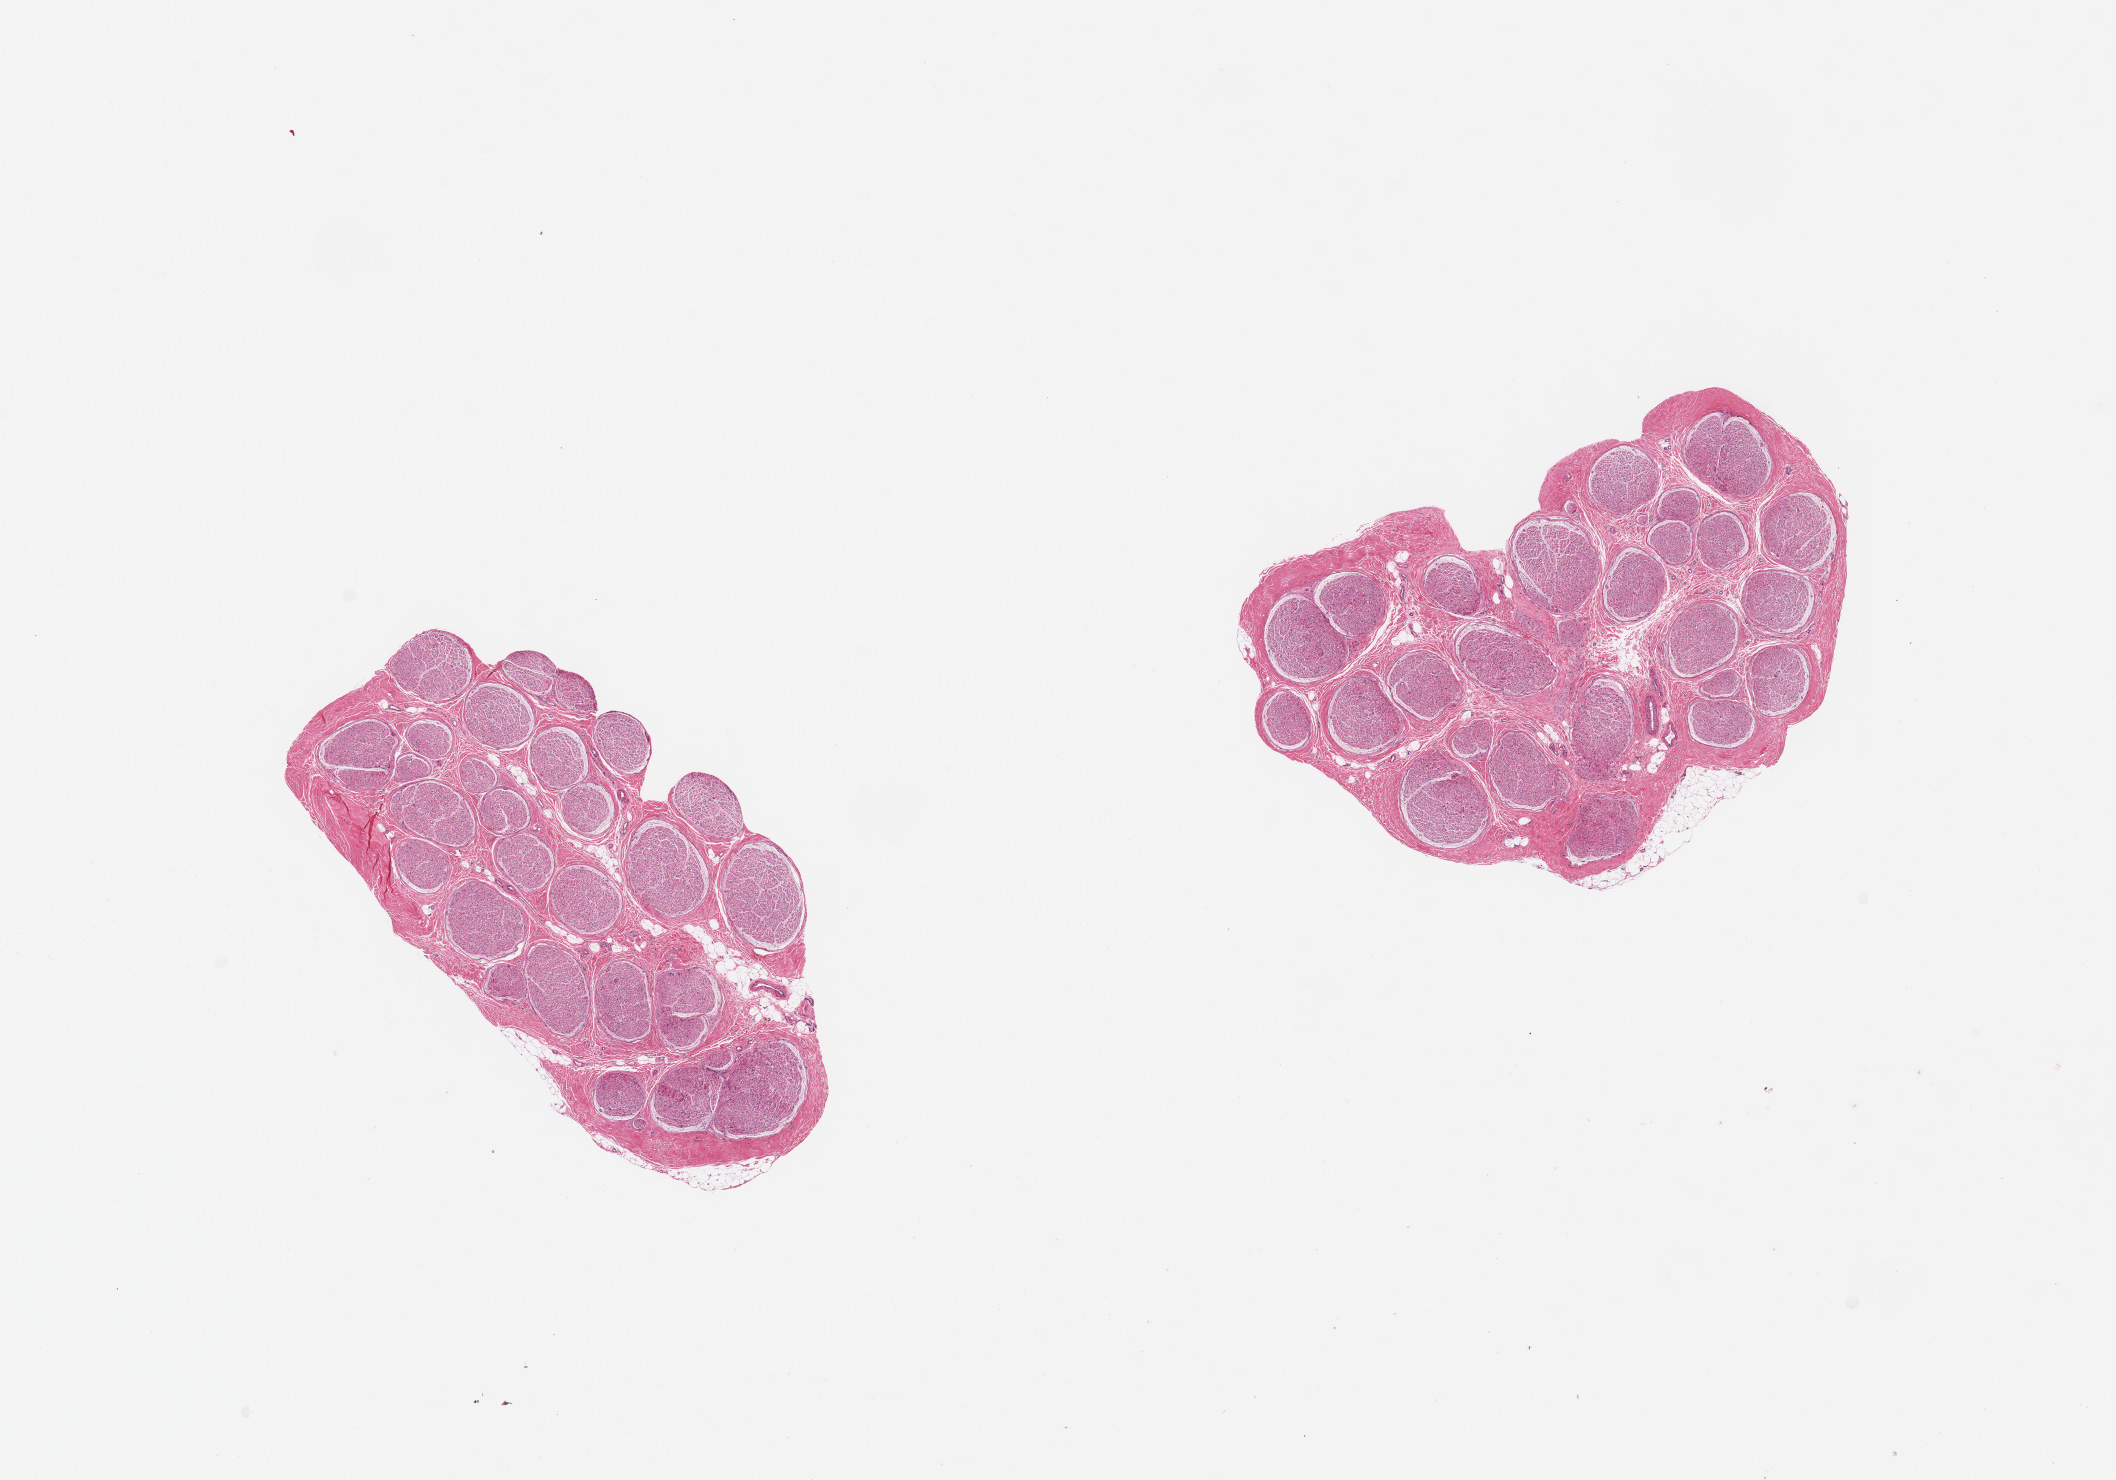
H&E whole-slide image, brightfield — whole scanned area (about 16.7 x 11.7 mm) shown as a low-resolution overview. PAXgene-fixed paraffin-embedded (PFPE) section. Sampled site (target tissue): tibial nerve. Tissue donor sample.
* review note (as recorded): 2 pieces; nerve fascicles surrounded by prineurium; trace of internal and external fat